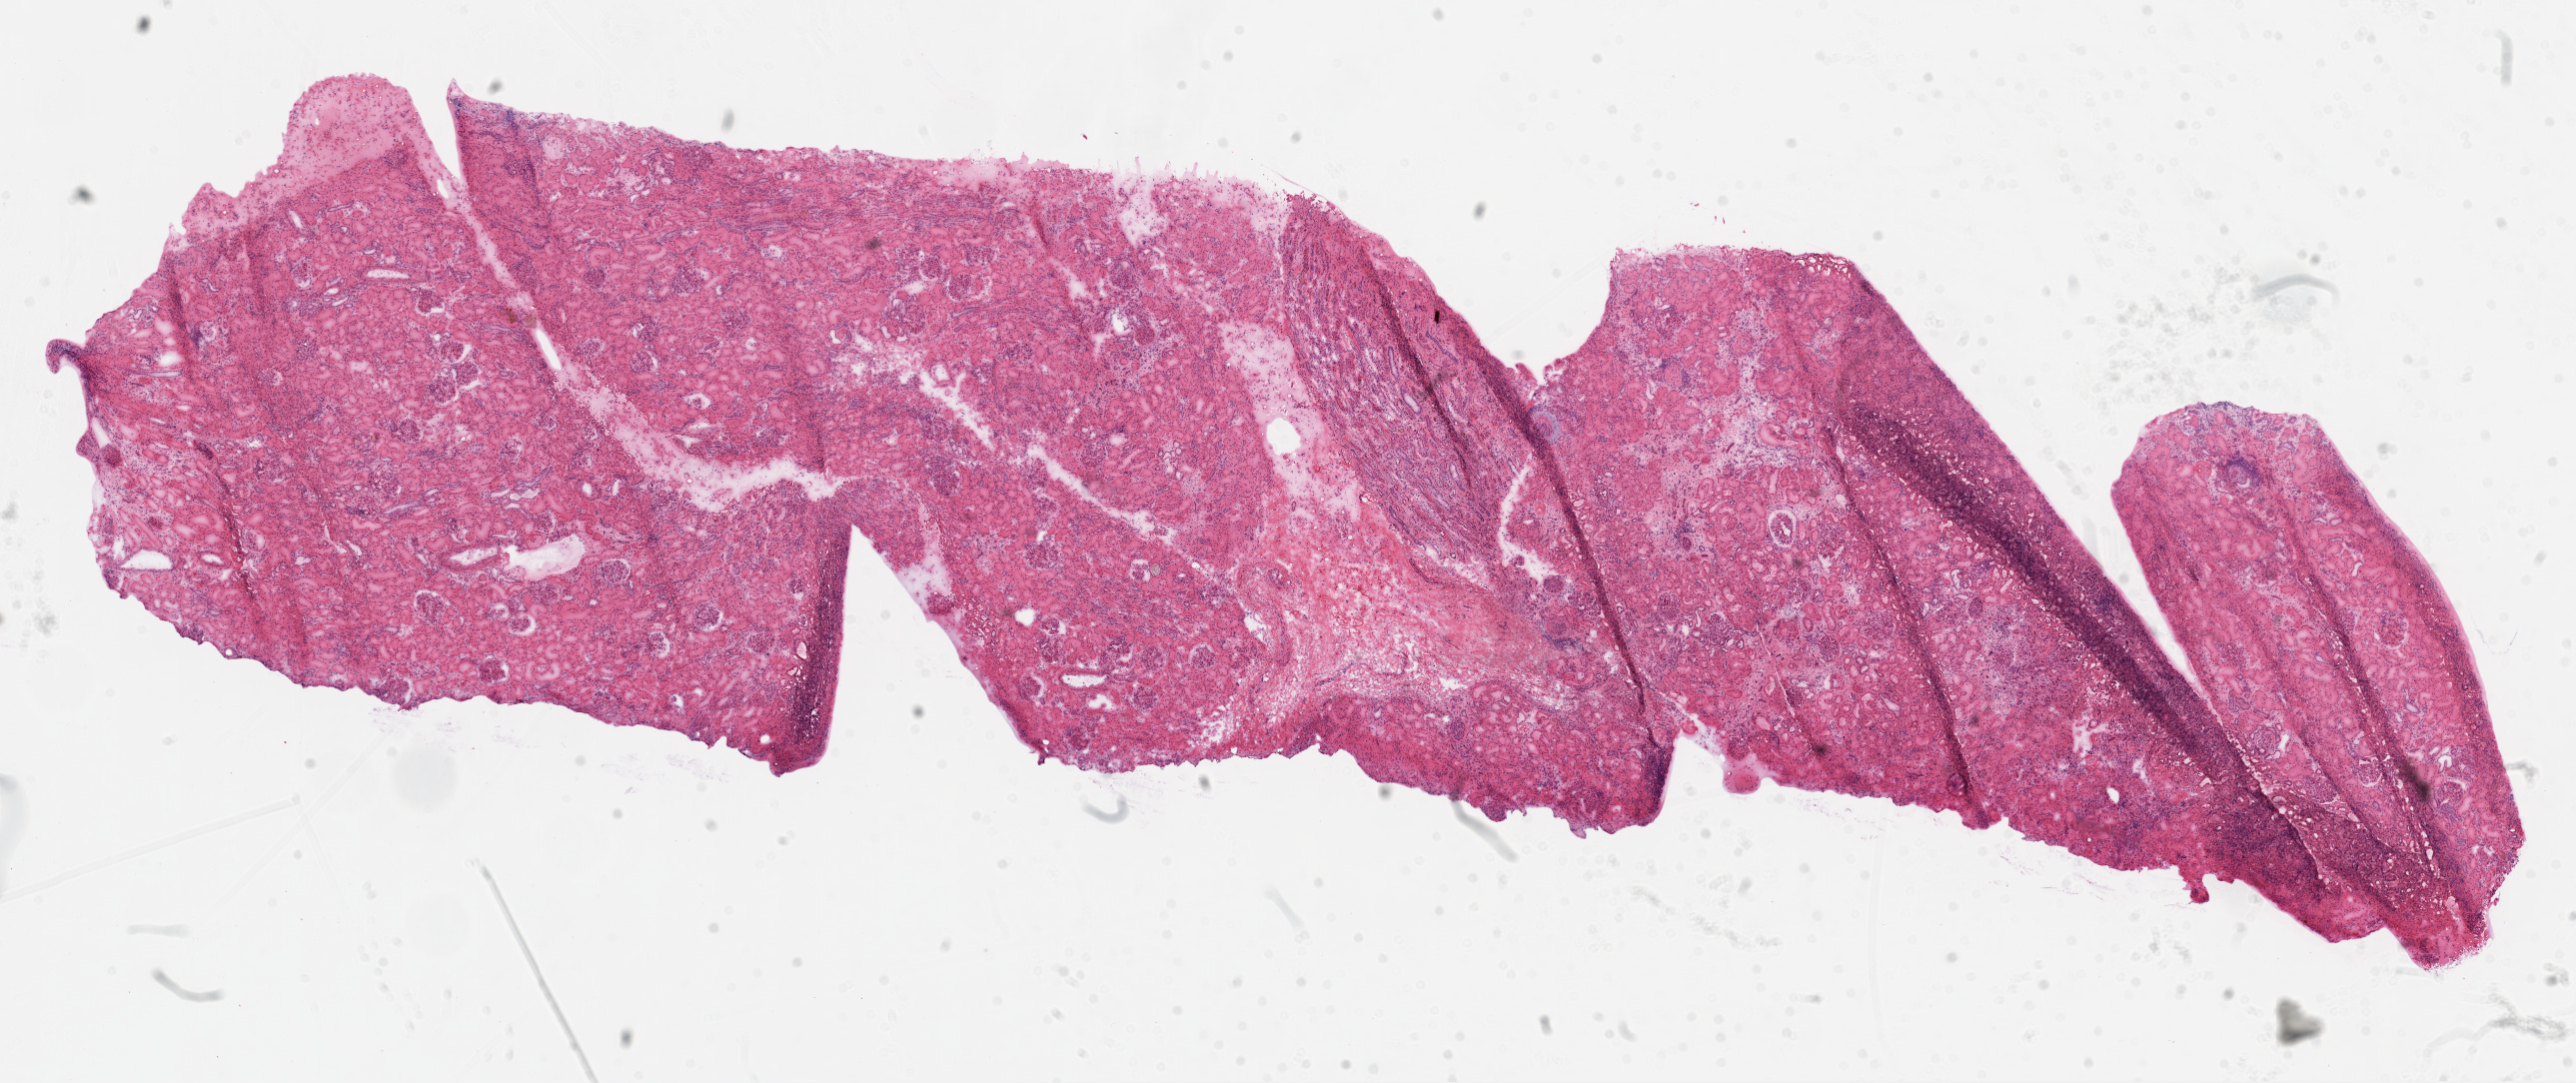
Whole-slide histology image, H&E, low-resolution overview of the scanned area, about 20.8 x 8.7 mm. Frozen section from the top of the tissue portion. Sample: solid tissue normal (non-tumour tissue), kidney. Male, age 60 years at initial diagnosis.
* this section: solid tissue normal sample (biorepository sample class)
* patient diagnosis: Clear cell adenocarcinoma, NOS